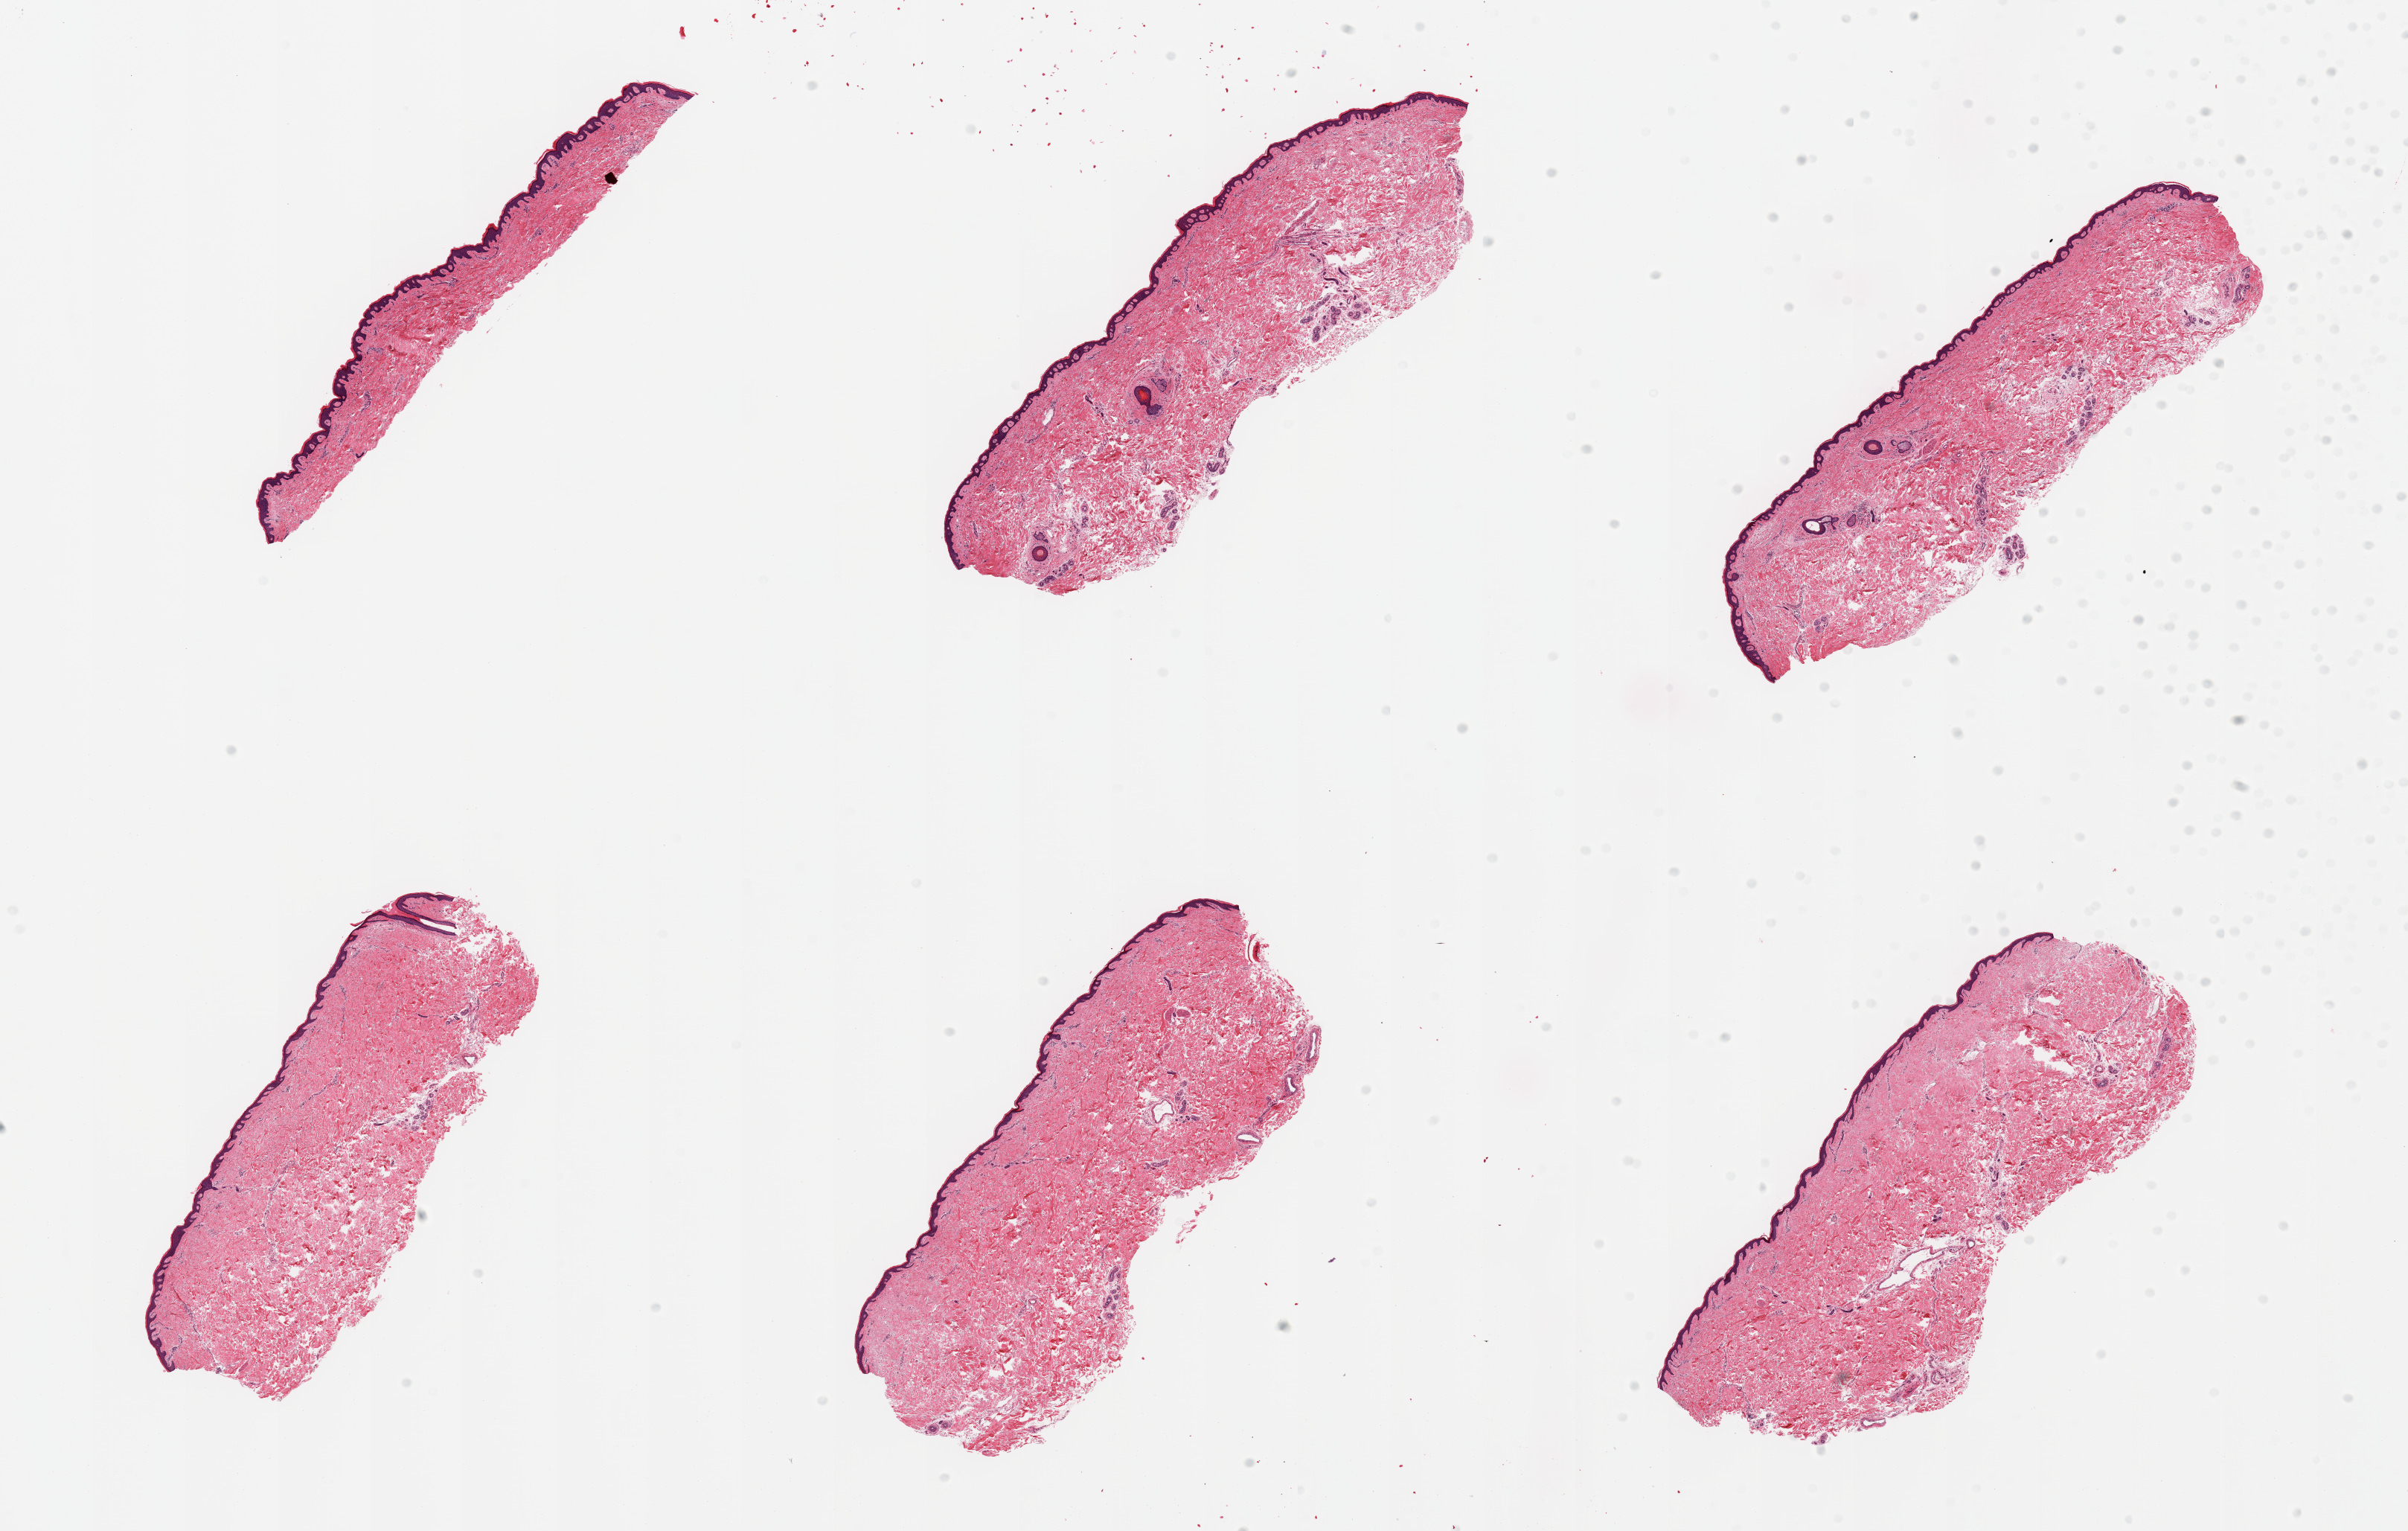
Whole-slide image, H&E stain, a low-resolution overview of the entire scanned area, about 25.6 x 16.3 mm (acquisition: 20x scan); PAXgene-fixed paraffin-embedded (PFPE) section; section of skin of lower leg (target tissue); tissue donor sample.
* pathologist's review note for this sample: 6 pieces; well trimmed, epidermis measures 45 microns